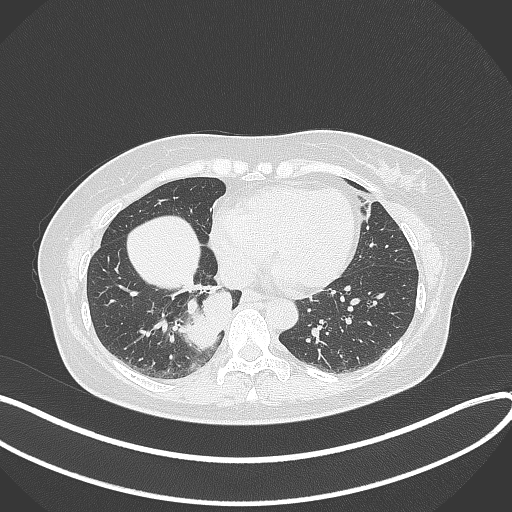
Chest CT, one axial slice. Slice 116 of 331 in the series (ordered by position). 120 kVp. Lung window (W 1500 / L -600 HU). 1 mm slice thickness. 512 × 512 image matrix. Female patient, age 54 years. Case-level facts recorded for this patient, not image findings: clinical TNM (as recorded): T4 N0 M0.
Structures marked on this image (rectangle marked by the reading radiologist):
- lung tumour (recorded histology: adenocarcinoma): bounding box (x1, y1, x2, y2) in pixels: (173, 283, 236, 355)